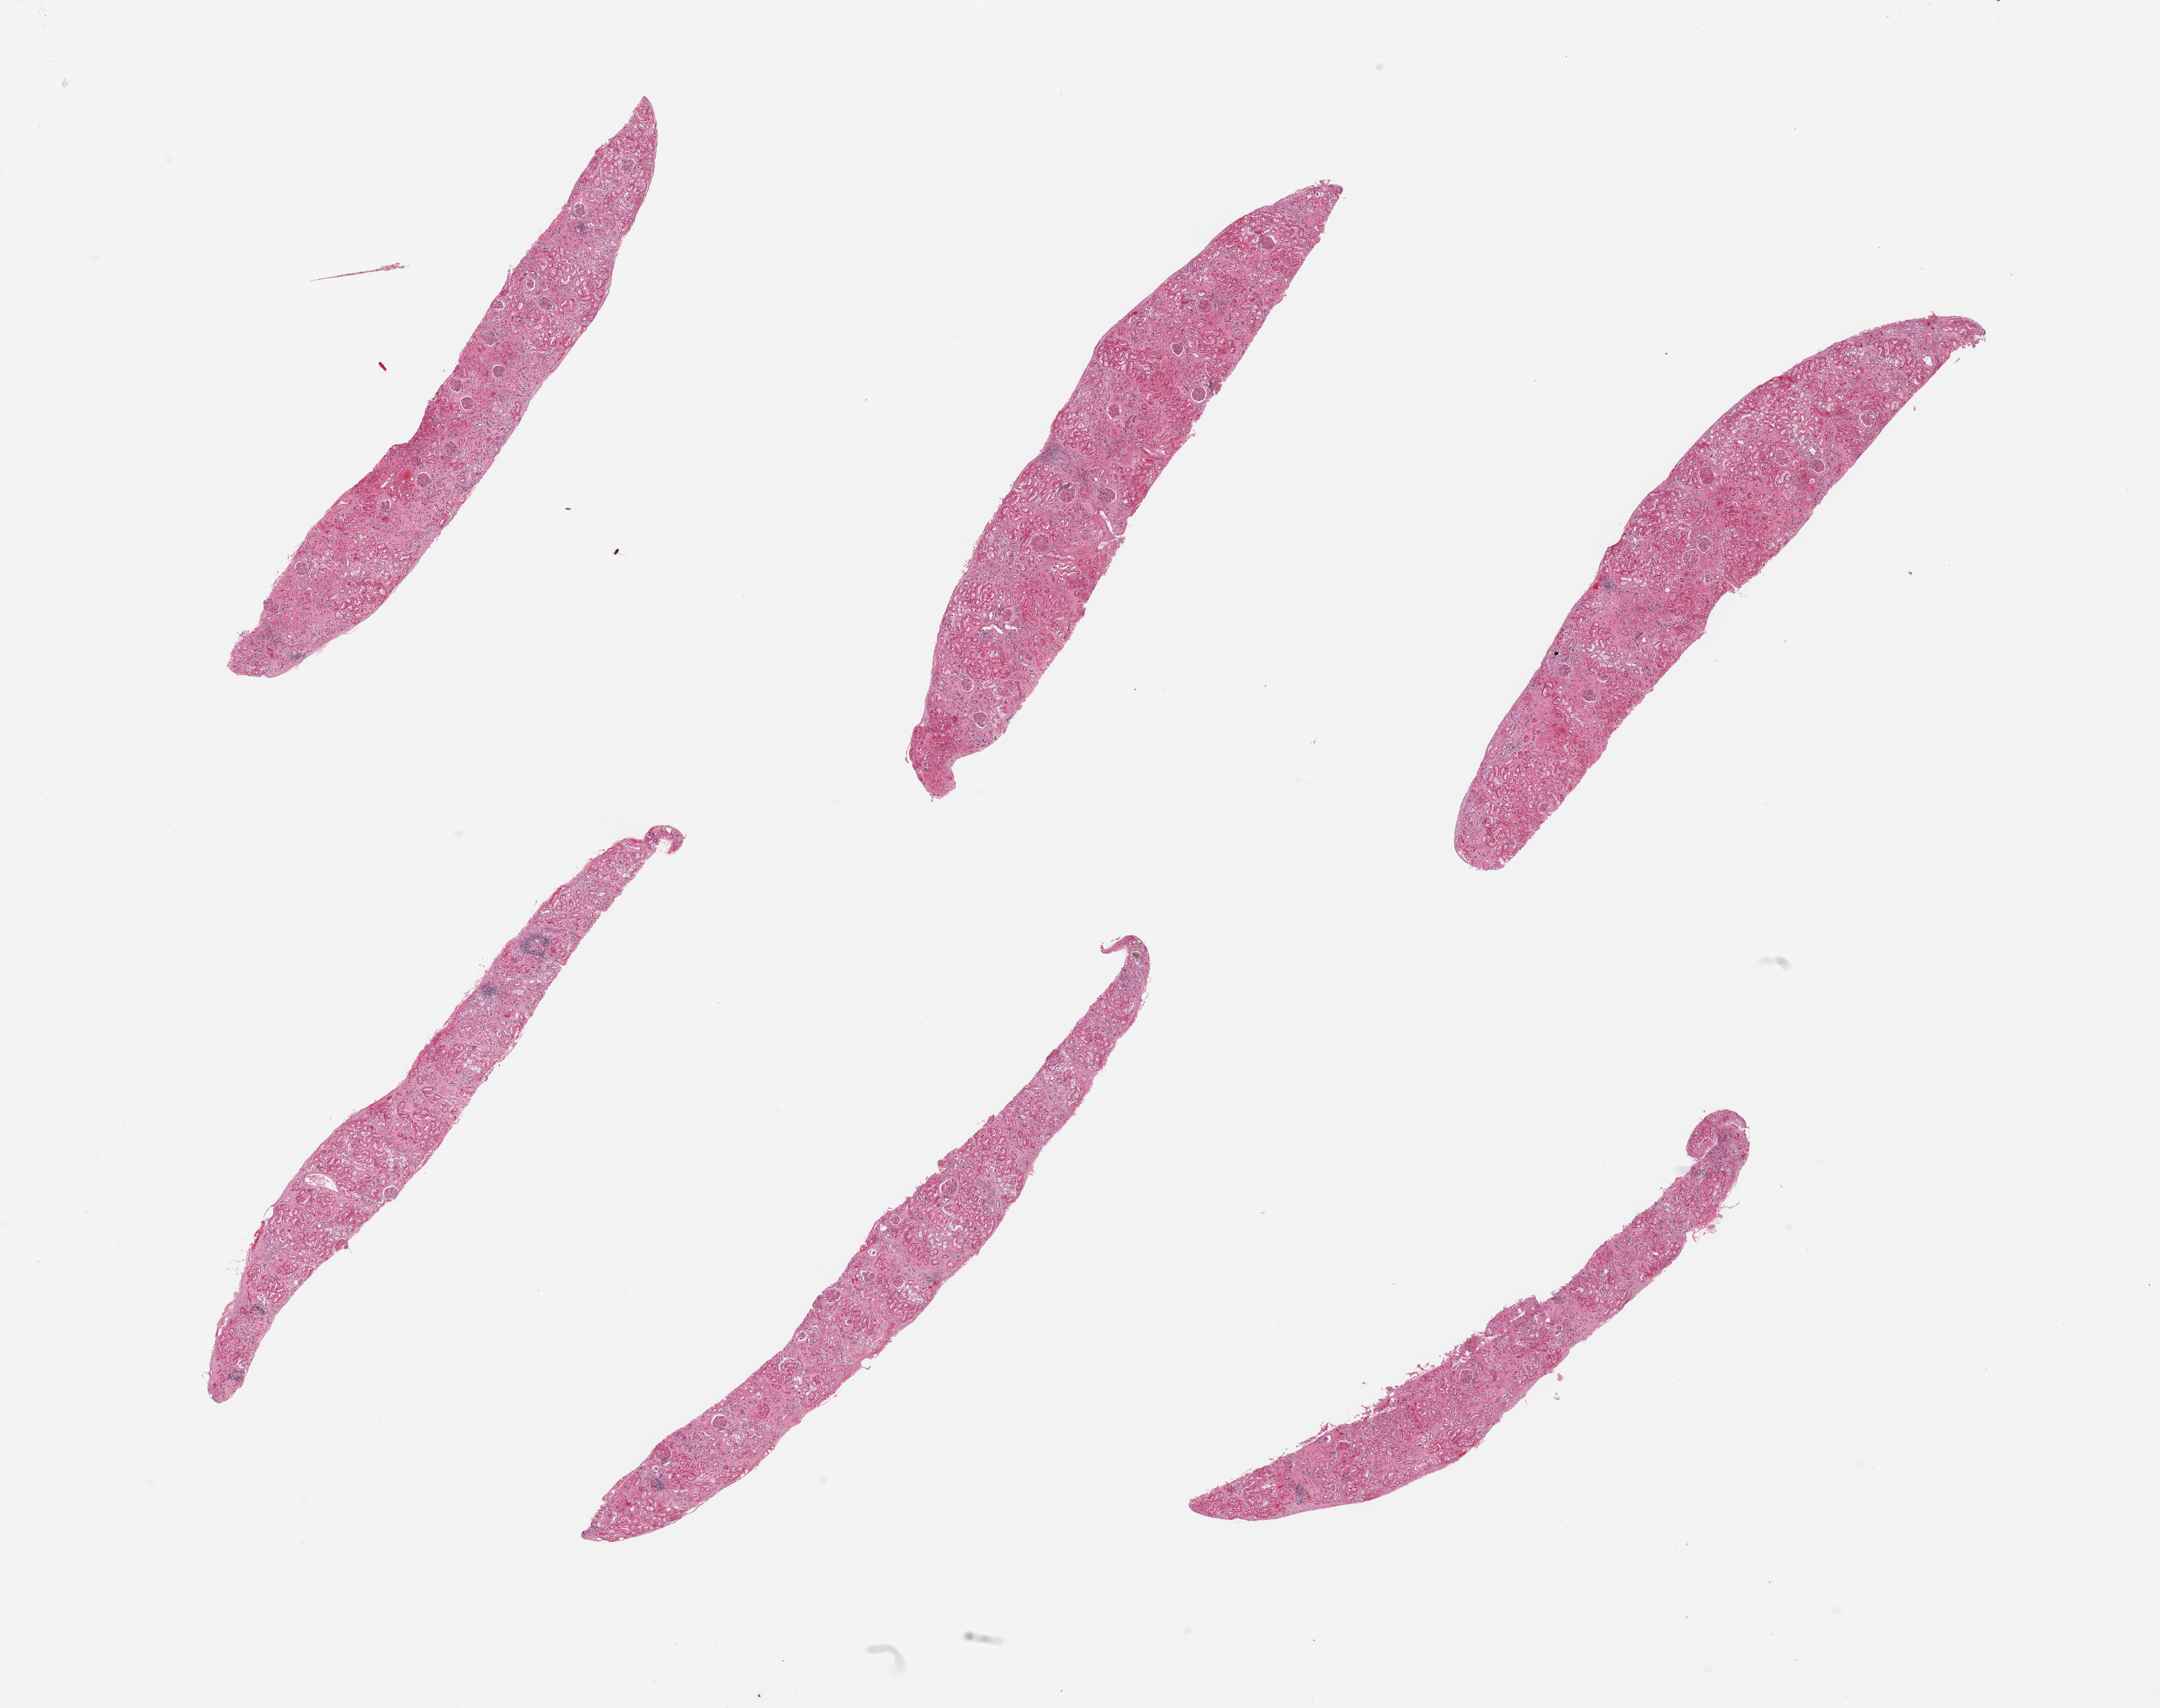
Digitized haematoxylin and eosin-stained section — a low-resolution overview of the entire scanned area, about 24.6 x 19.5 mm, PAXgene-fixed, paraffin-embedded tissue, target tissue: renal cortex, tissue donor sample. Donor: male.
Review note (as recorded): 6 pieces; moderate interstitial fibrosis; tubules severely autolyzed.